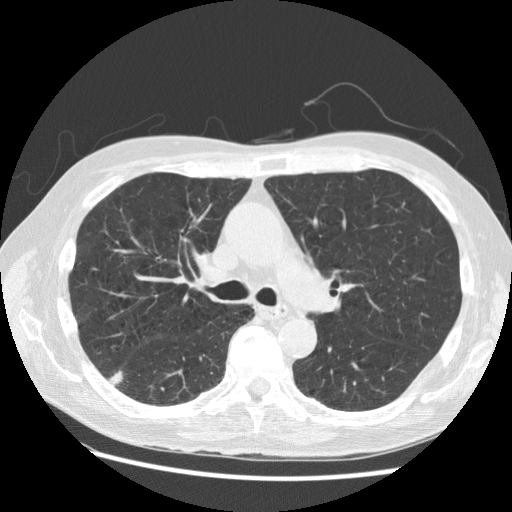
Low-dose screening chest CT, one axial slice. Slice 103 of 168 in the series (ordered by position). Reconstruction kernel STANDARD. 120 kVp. Lung window (W 1500 / L -600 HU). 2.5 mm slice thickness. 512 × 512 image matrix, field of view 360 × 360 mm.
Outlined on this slice (manually delineated by an expert):
- lesion 1 (tumor, lower lobe of right lung): bounding box <112,373,122,383> (left, top, right, bottom; pixels)